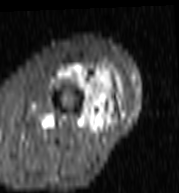
MRI of an extremity soft-tissue mass, one axial slice; position 38 of 103 along the scan axis; STIR; MR volume resampled by the dataset authors to the PET/CT grid (not the native acquisition matrix); 3.27 mm slice thickness; 179 × 193 image matrix, field of view 175 × 188 mm. Female patient. From the clinical record (not read from this slice): histological type: undifferentiated – high grade; grade: high; site of the primary tumour: left thigh.
Structures marked on this image (expert contour drawn on MRI and transferred to this co-registered scan by the dataset authors):
- gross tumour volume including surrounding oedema: bounding box (x1, y1, x2, y2) in pixels: (59, 64, 122, 129)
- gross tumour volume (mass): (102, 78, 108, 81)